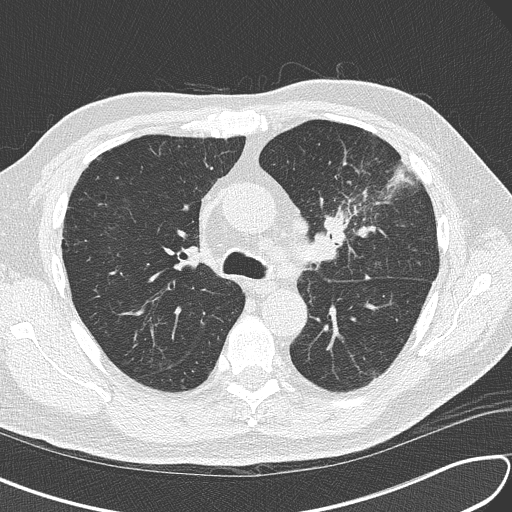
Low-dose screening chest CT, axial slice, third screening round (two years after baseline), lung window (W 1500 / L -600 HU), 2 mm slice thickness, lung (sharp) reconstruction kernel (B50f). Male participant, aged 67 years at enrolment.
Lesion marked by an expert reader, bounding box [x1, y1, x2, y2] px = [298, 175, 399, 270]. Screening reader's record for this exam (one nodule recorded; not confirmed to be the boxed lesion): non-calcified nodule or mass ≥4 mm, left upper lobe, 30 × 23 mm, soft tissue attenuation, pre-existing on the prior screen: no. Later outcome: lung cancer diagnosed 41 days after this screen — small cell carcinoma, NOS, left upper lobe, stage IV (AJCC 6th edition), 30 mm at pathology.